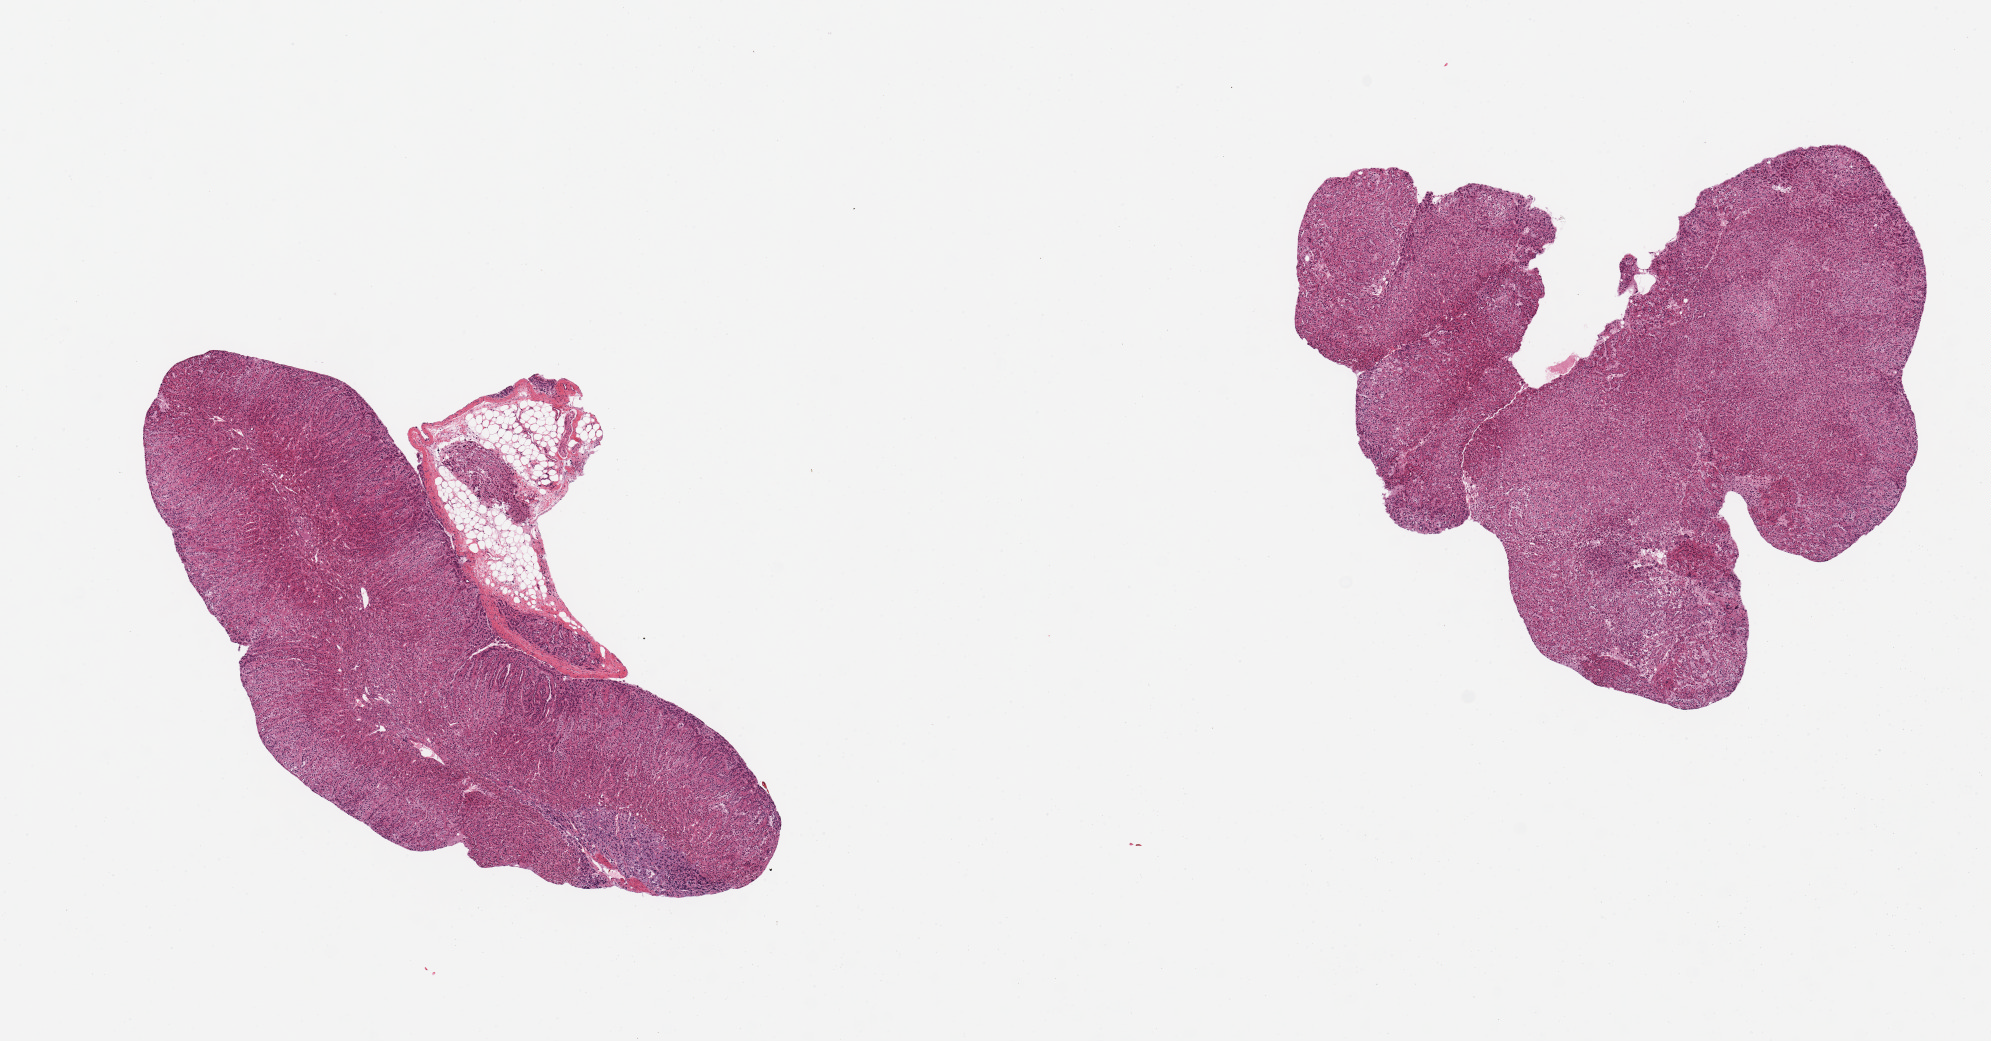
Whole-slide image, H&E stain, a low-resolution overview of the entire scanned area, about 15.8 x 8.2 mm, PAXgene-fixed, paraffin-embedded tissue, sampled site (target tissue): adrenal gland, donor tissue sample. Female donor.
Reviewer comment on this tissue sample: 2 pieces, mainly cortex; ~1x0.4mm focus of medualla; nubbin of adherent fat.